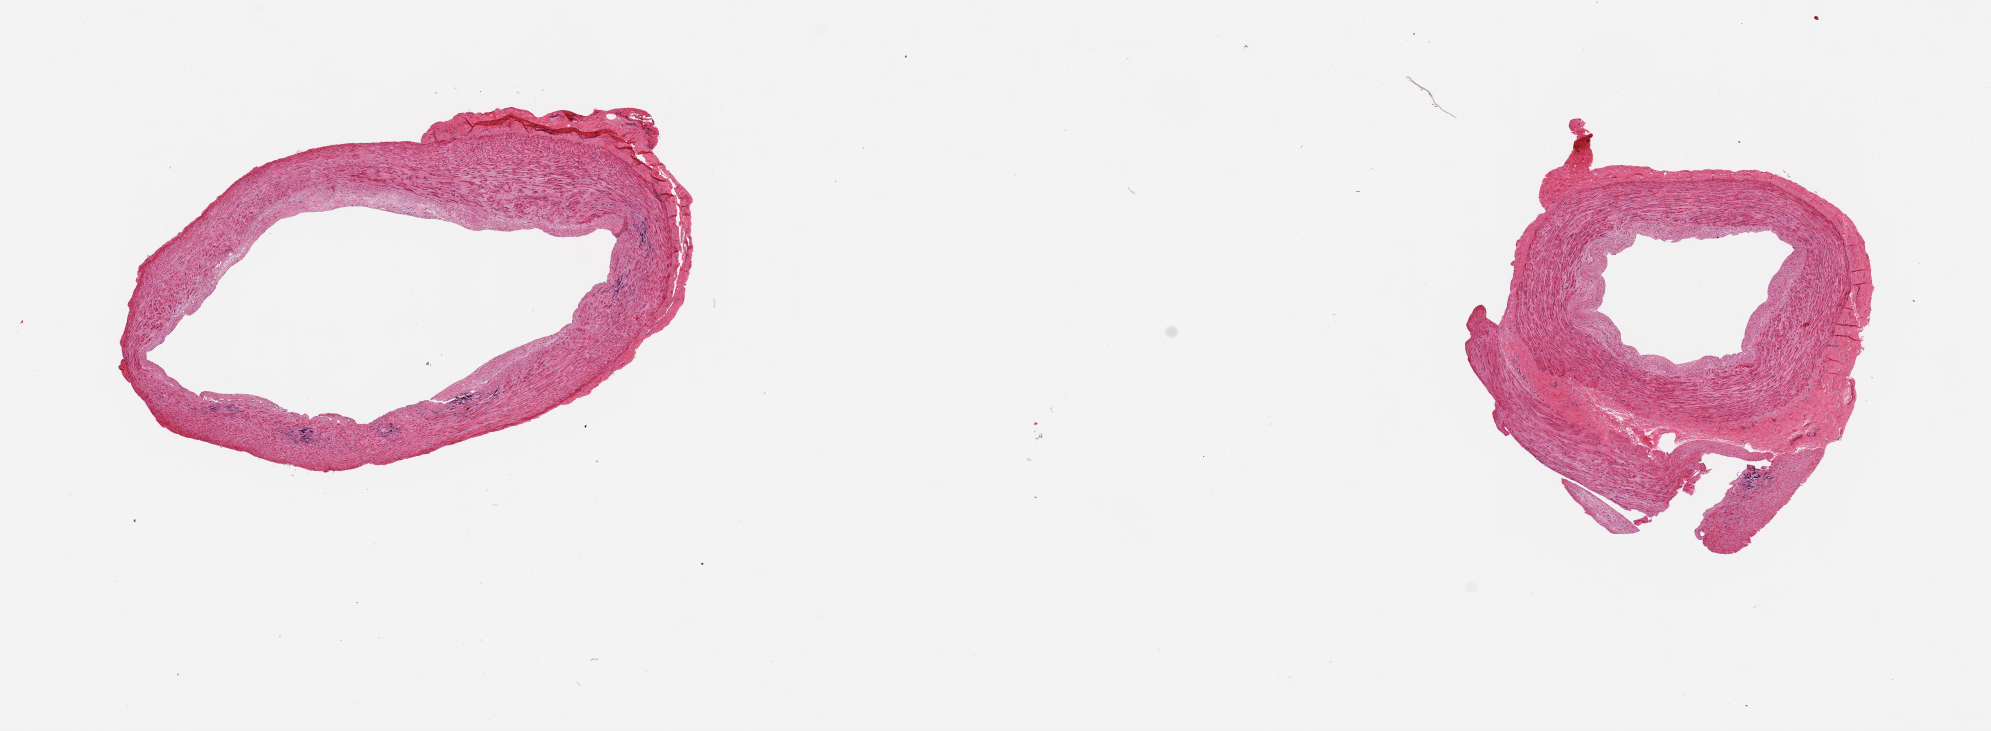
Digitized hematoxylin and eosin (H&E)-stained section, brightfield — a low-resolution overview of the entire scanned area, about 15.8 x 5.8 mm. Donor: male.
* specimen: PAXgene-fixed, paraffin-embedded tissue; target tissue: tibial artery; donor tissue sample